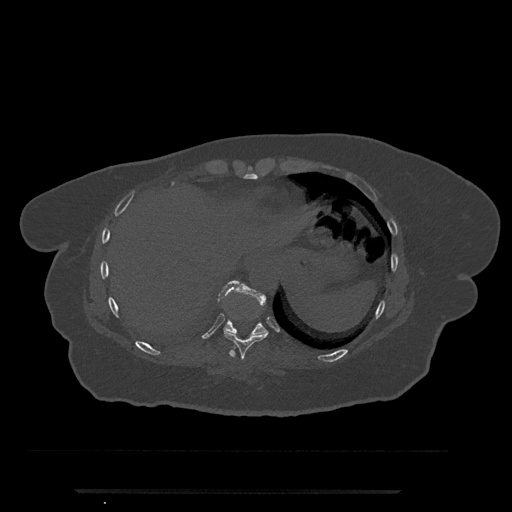
CT including the spine, one axial slice. Reconstruction kernel Br40s/3. 120 kVp. Bone window (W 1800 / L 400 HU). 0.5 mm slice thickness. 512 × 512 image matrix, field of view 440 × 440 mm. Female patient, age 51 years. From the clinical record (not read from this slice): primary cancer: neuro.
Annotated regions visible in this slice (semi-automatically segmented with operator editing):
- T10 vertebra: bounding box <218,280,266,336> (left, top, right, bottom; pixels)
- T9 vertebra: <224,330,268,359>